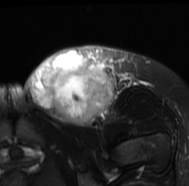
MRI of an extremity soft-tissue mass, one axial slice. Slice 42 of 77 in the series (ordered by position). T2-weighted fat-saturated. MR volume resampled by the dataset authors to the PET/CT grid (not the native acquisition matrix). 3.27 mm slice thickness. 189 × 186 image matrix, field of view 185 × 182 mm. Female patient. Case-level facts recorded for this patient, not image findings: histological type: leiomyosarcoma; grade: high; site of the primary tumour: groin.
Annotated regions visible in this slice (expert contour drawn on MRI and transferred to this co-registered scan by the dataset authors):
- gross tumour volume including surrounding oedema: bounding box (x1, y1, x2, y2) in pixels: (24, 45, 139, 130)
- gross tumour volume (mass): (26, 50, 114, 126)